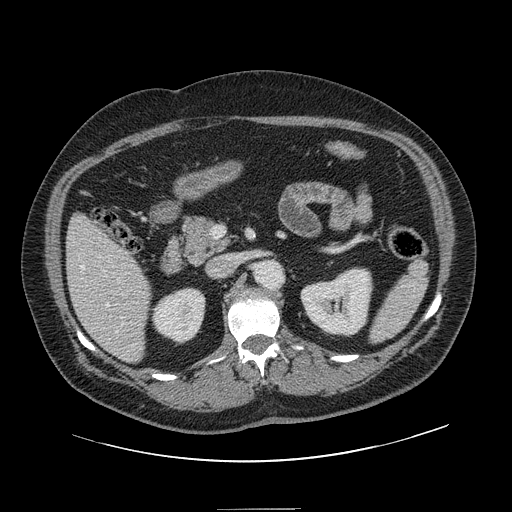
Contrast-enhanced abdominal CT, one axial slice. Slice 63 of 154 in the series (ordered by position). 120 kVp. Intravenous contrast given. Soft-tissue window (W 400 / L 40 HU). 512 × 512 image matrix. Male patient, age 61 years. From the clinical record (not read from this slice): diagnosis: colorectal cancer liver metastases, imaged before liver resection.
Outlined on this slice (expert manual segmentation):
- hepatic veins: box from (x=80, y=265) to (x=118, y=333) px
- liver: (x=68, y=216)–(x=151, y=362)
- planned liver remnant (the part of the liver to remain after resection): (x=68, y=215)–(x=151, y=362)